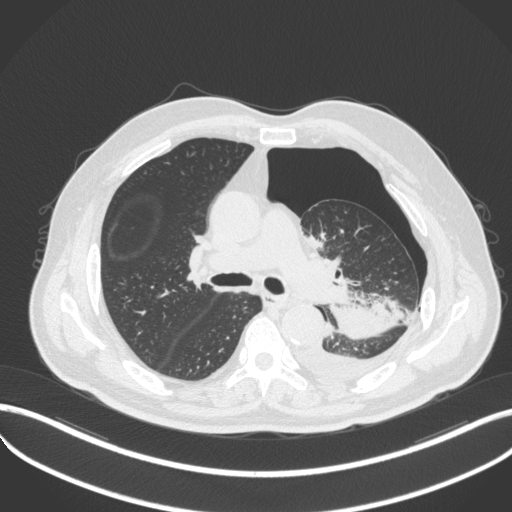
Chest CT, one axial slice; slice 319 of 466 in the series (ordered by position); reconstruction kernel B31f; lung window (W 1500 / L -600 HU); 1 mm slice thickness; 512 × 512 image matrix, field of view 400 × 400 mm. Patient: male, 76 years. From the clinical record (not read from this slice): clinical TNM (as recorded): T3 N0 M1b.
Annotated regions visible in this slice (bounding box drawn by a radiologist):
- lung tumour (recorded histology: adenocarcinoma): bounding box [x1, y1, x2, y2] px = [323, 281, 407, 345]